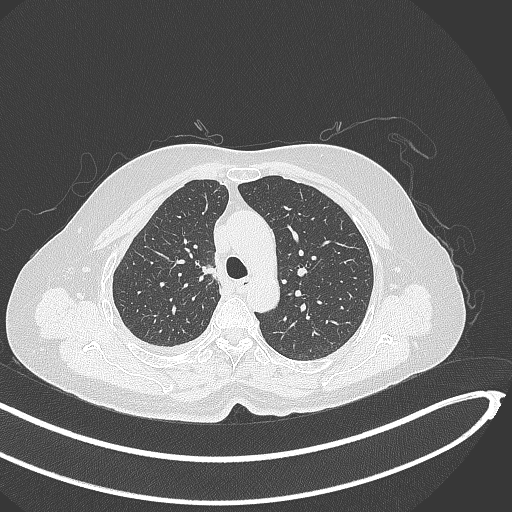
Chest CT, one axial slice. Slice 270 of 345 in the series (ordered by position). Reconstruction kernel B70f. 120 kVp. Lung window (W 1500 / L -600 HU). 512 × 512 image matrix. Female patient, age 64 years. Case-level facts recorded for this patient, not image findings: clinical TNM (as recorded): T1b N0 M1.
Structures marked on this image (rectangle marked by the reading radiologist):
- lung tumour (recorded histology: adenocarcinoma): bounding box [x1, y1, x2, y2] px = [198, 258, 220, 282]